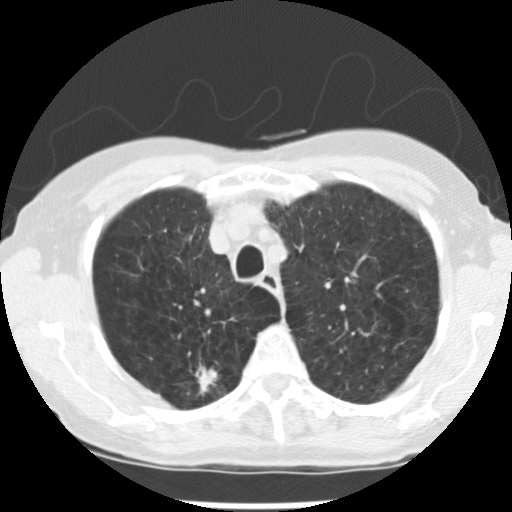
Axial slice from a low-dose chest CT screening exam; baseline annual screen; lung window (W 1500 / L -600 HU); 2.5 mm slice thickness; standard (soft-tissue) reconstruction kernel (STANDARD); slice 50 of 265 in the series. Female, age 72 years at enrolment. Current smoker at enrolment.
Lesion marked by an expert reader, bounding box <183,360,235,406> (left, top, right, bottom; pixels). The screening reader recorded 3 non-calcified nodules or masses ≥4 mm on this exam (right upper lobe, left upper lobe, left lower lobe); which of them this box marks is not recorded. Official screen result: positive, change unspecified: nodule(s) >= 4 mm or enlarging nodule(s), mass(es), or other non-specific abnormalities suspicious for lung cancer.